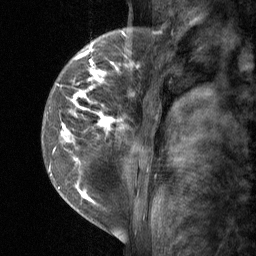
Breast MRI (dynamic contrast-enhanced), one sagittal slice. Slice 15 of 64 in the series (ordered by position). Dynamic contrast-enhanced study with each time point stored as its own series, time point 2 of 3 at this slice position (early post-contrast, ordered by acquisition time). 1.5 T. TE 4.8 ms, TR 27 ms. 256 × 256 image matrix, field of view 180 × 180 mm. Female patient, age 34 years. From the clinical record (not read from this slice): setting: breast cancer imaged before/during neoadjuvant chemotherapy; receptor status: HR-positive, HER2-negative.
Outlined on this slice (semi-automatic segmentation, software-assisted and operator-edited):
- analysis volume of interest (the breast-tissue region the enhancement analysis was run in; not a lesion): bounding box <41,23,157,197> (left, top, right, bottom; pixels)
- tumour enhancement mask (voxels above the 90 % enhancement threshold inside the analysis volume of interest): <50,33,156,197>